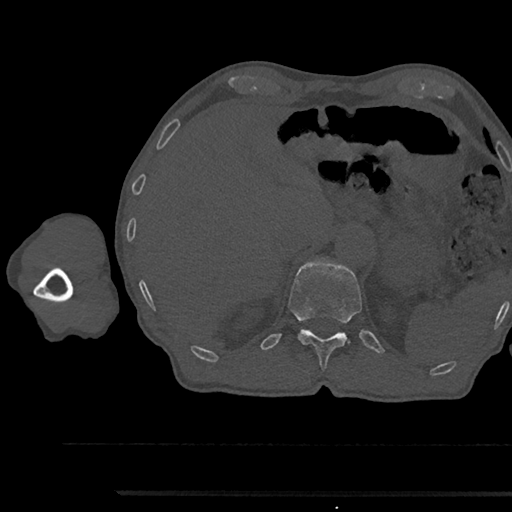
CT including the spine, one axial slice. Slice 707 of 797 in the series (ordered by position). 120 kVp. Bone window (W 1800 / L 400 HU). 0.5 mm slice thickness. 512 × 512 image matrix, field of view 367 × 367 mm. Patient: male, 79 years. Case-level facts recorded for this patient, not image findings: primary cancer: prostate.
Annotated regions visible in this slice (semi-automatic segmentation, software-assisted and operator-edited):
- T12 vertebra: bounding box <288,260,362,370> (left, top, right, bottom; pixels)